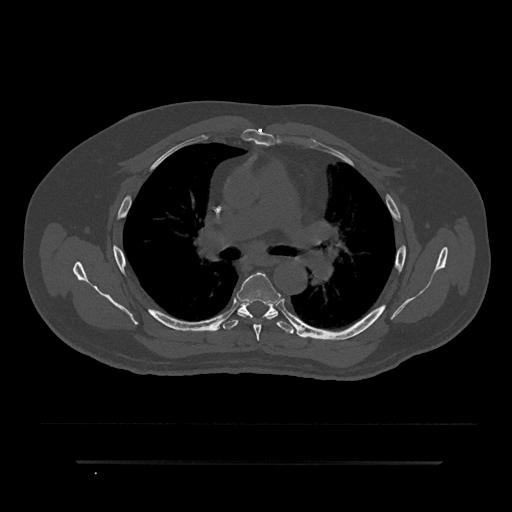
CT including the spine, one axial slice. Position 555 of 797 along the scan axis. Reconstruction kernel Br40s/3. 120 kVp. Bone window (W 1800 / L 400 HU). 0.5 mm slice thickness. 512 × 512 image matrix, field of view 464 × 464 mm. Patient: male, 59 years. From the clinical record (not read from this slice): primary cancer: bile ducts.
Structures marked on this image (semi-automatically segmented with operator editing):
- T5 vertebra: bounding box [x1, y1, x2, y2] px = [237, 272, 278, 341]
- T6 vertebra: [221, 299, 294, 334]